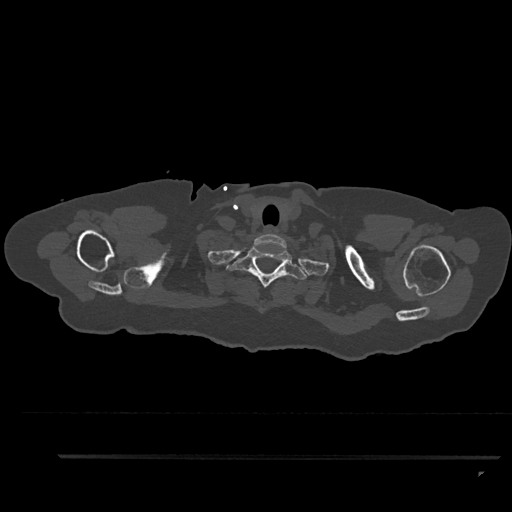
CT including the spine, one axial slice. Slice 768 of 797 in the series (ordered by position). Bone window (W 1800 / L 400 HU). 0.5 mm slice thickness. 512 × 512 image matrix, field of view 408 × 408 mm. Patient: female, 44 years. Case-level facts recorded for this patient, not image findings: primary cancer: renal.
Structures marked on this image (semi-automatic segmentation, software-assisted and operator-edited):
- T1 vertebra: bounding box [x1, y1, x2, y2] px = [226, 246, 308, 288]